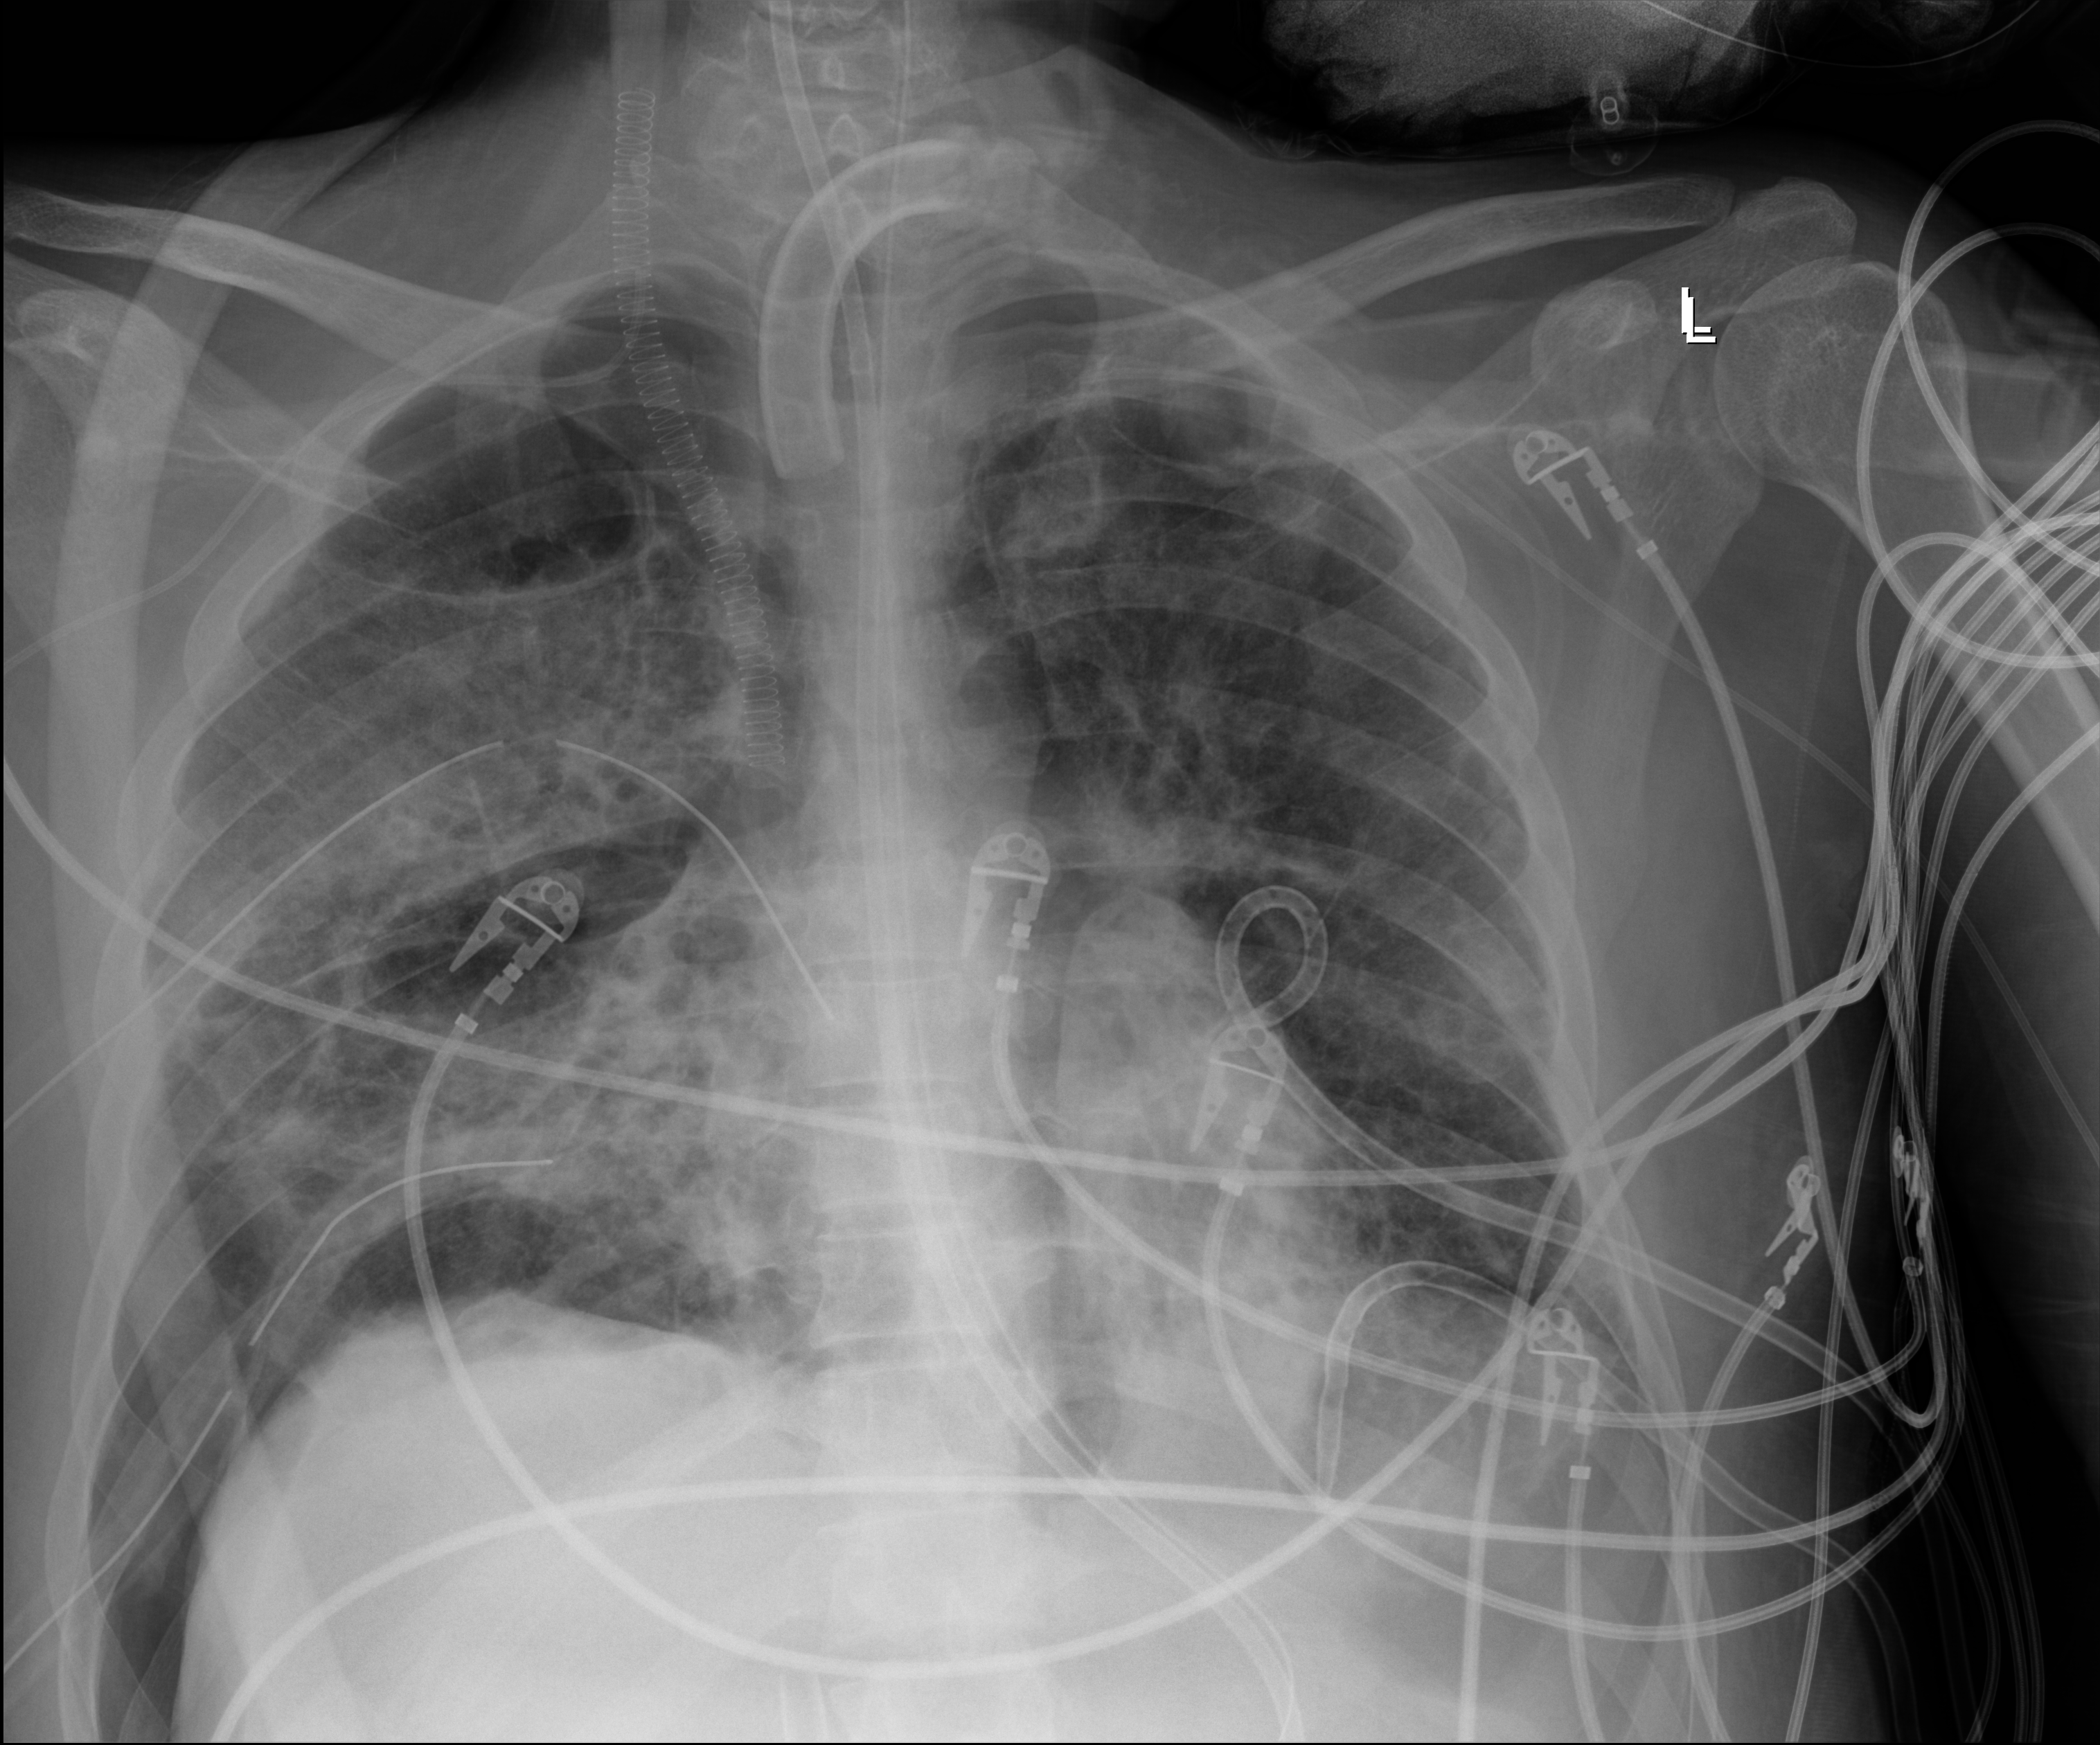
Bedside chest radiograph (digital radiography); anteroposterior (AP) projection. Patient hospitalised with COVID-19, aged 18–59 years.
Hospital-stay facts (about this admission, not read from this image; timing relative to this image not recorded): diabetes (admission record): no; mechanically ventilated during this hospital stay: yes.